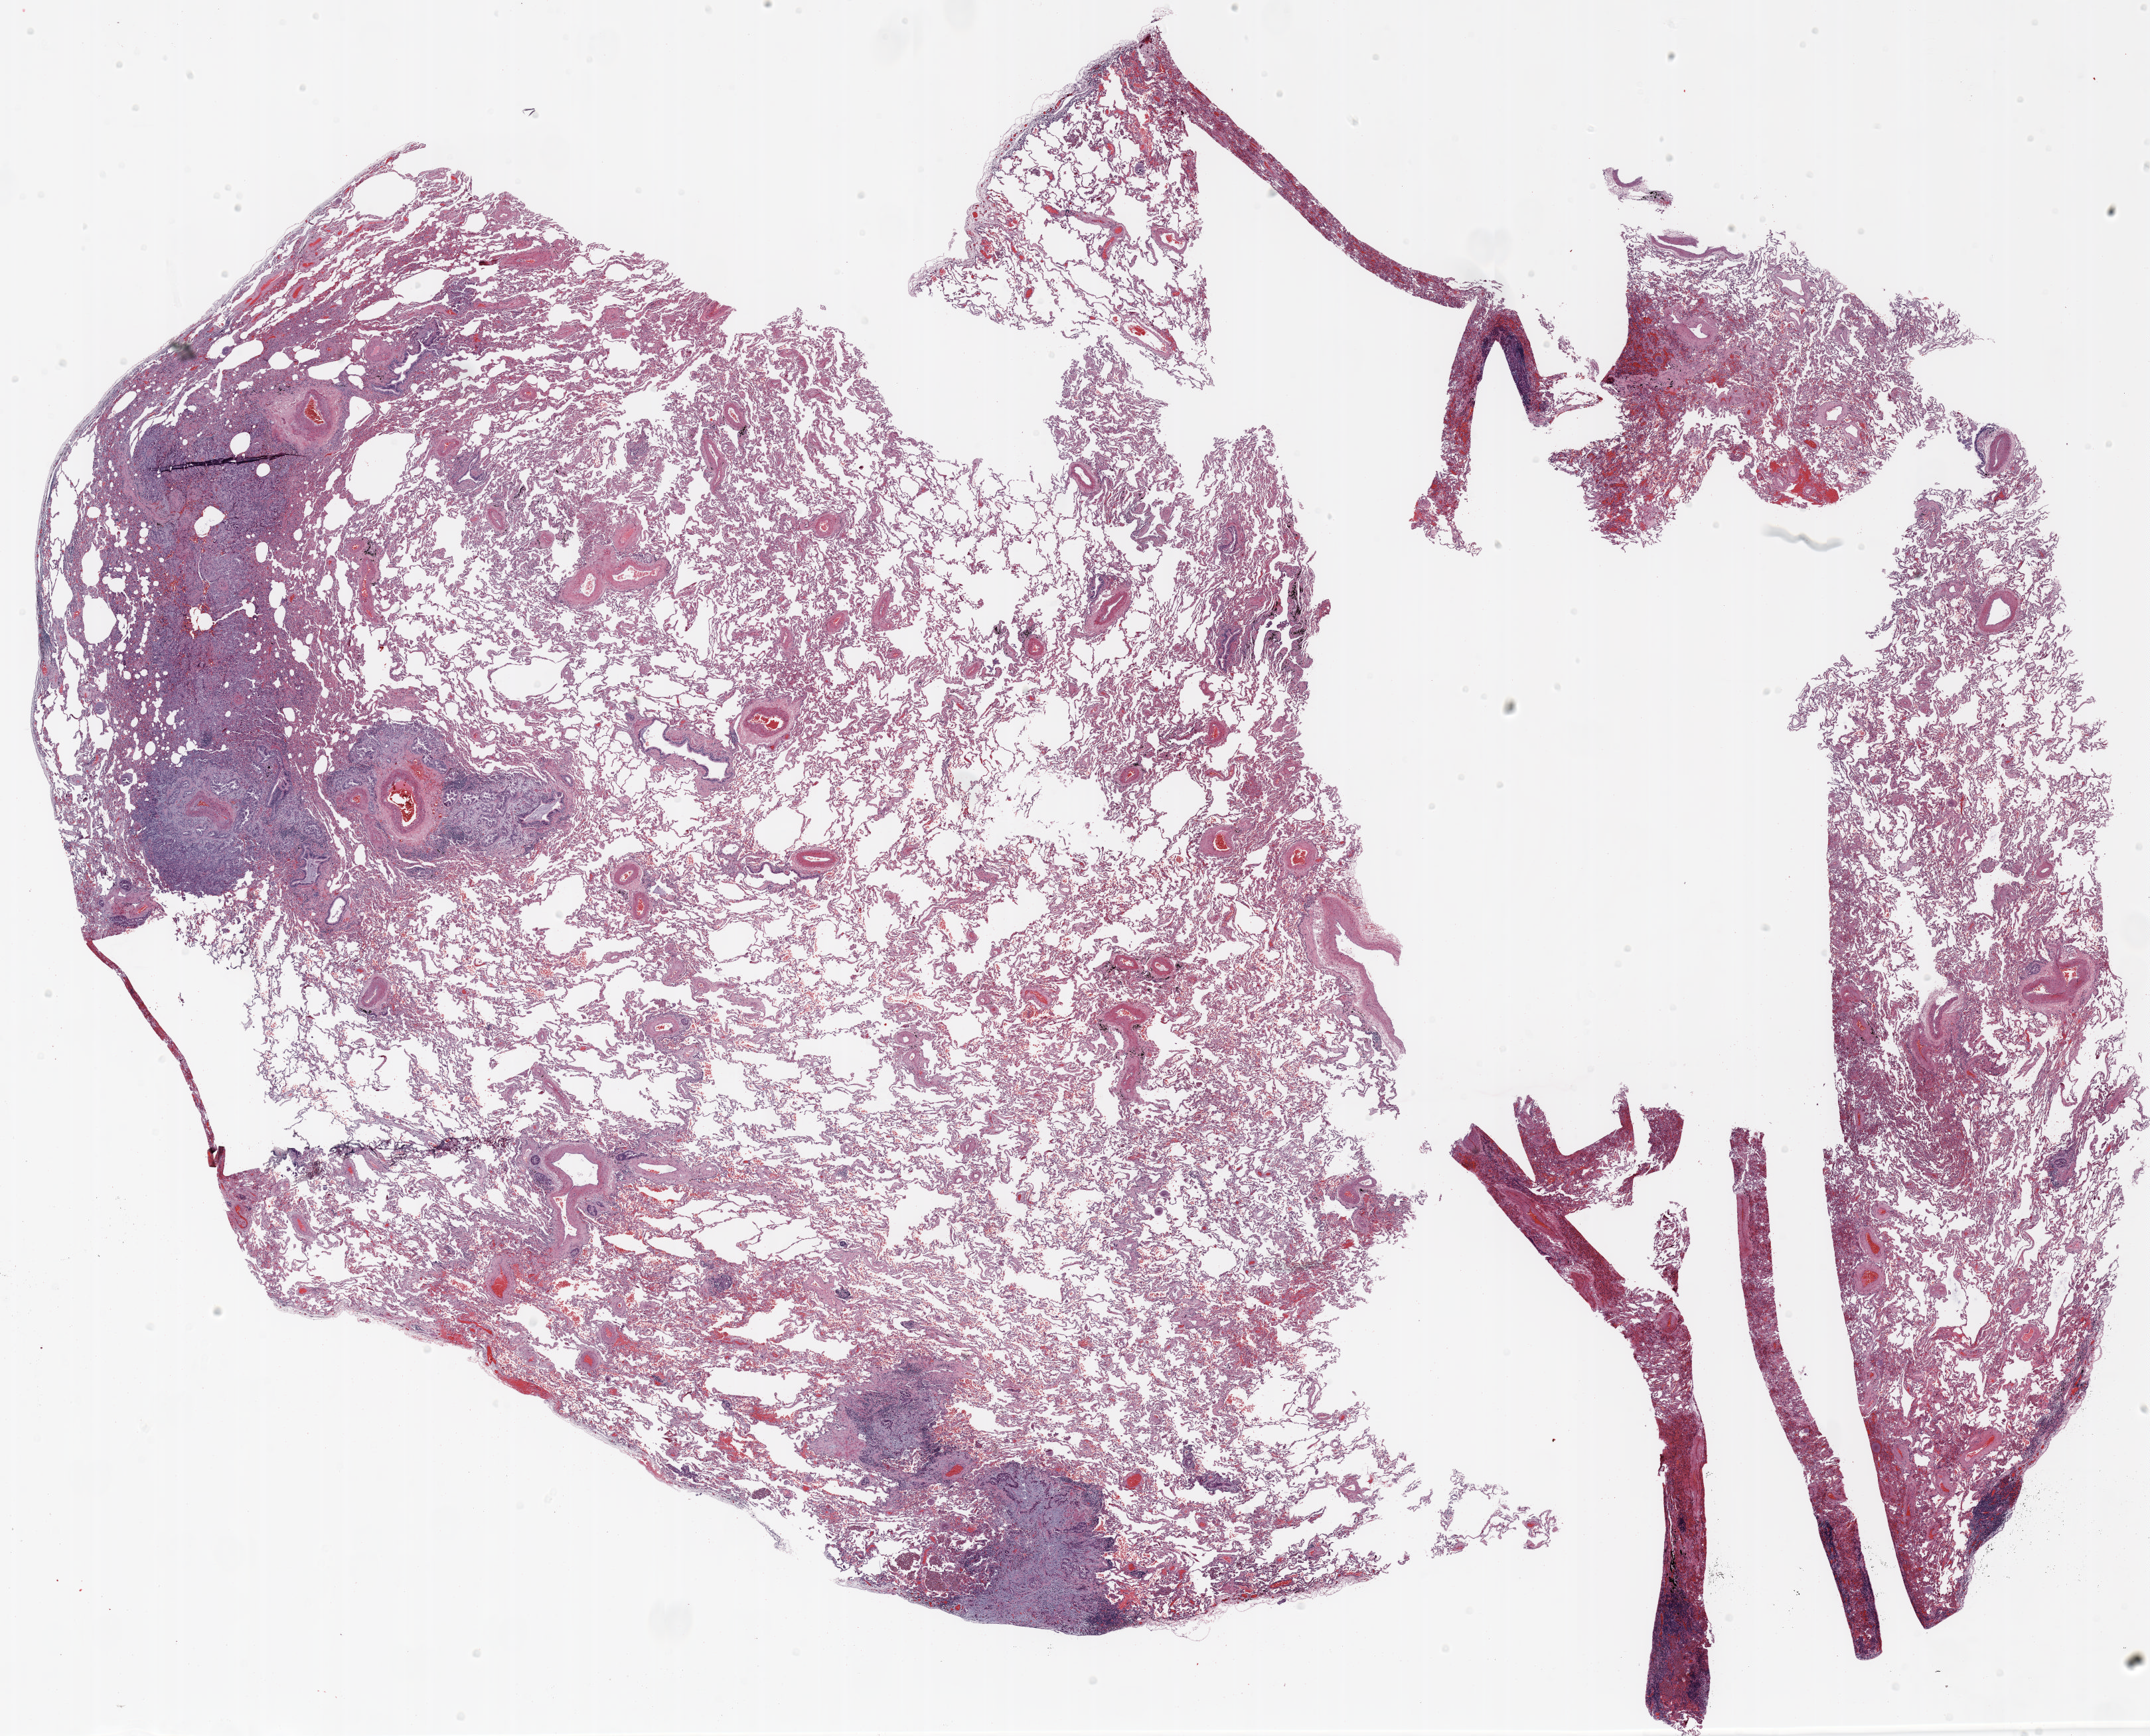
Whole-slide histology image, H&E-stained — shown as a low-resolution overview of the whole scanned area (about 26.0 x 21.0 mm), FFPE section, lung. Female, age 73 at enrolment. Current smoker at enrolment. Grade: moderately differentiated (G2).
Primary tumour location (clinical record): left upper lobe. Tumour size (pathology): 12 mm. ICD-O-3 topography: upper lobe of lung (C34.1). Stage (AJCC 6th edition): IIIB. Participant's lung-cancer diagnosis: Adenocarcinoma, NOS.